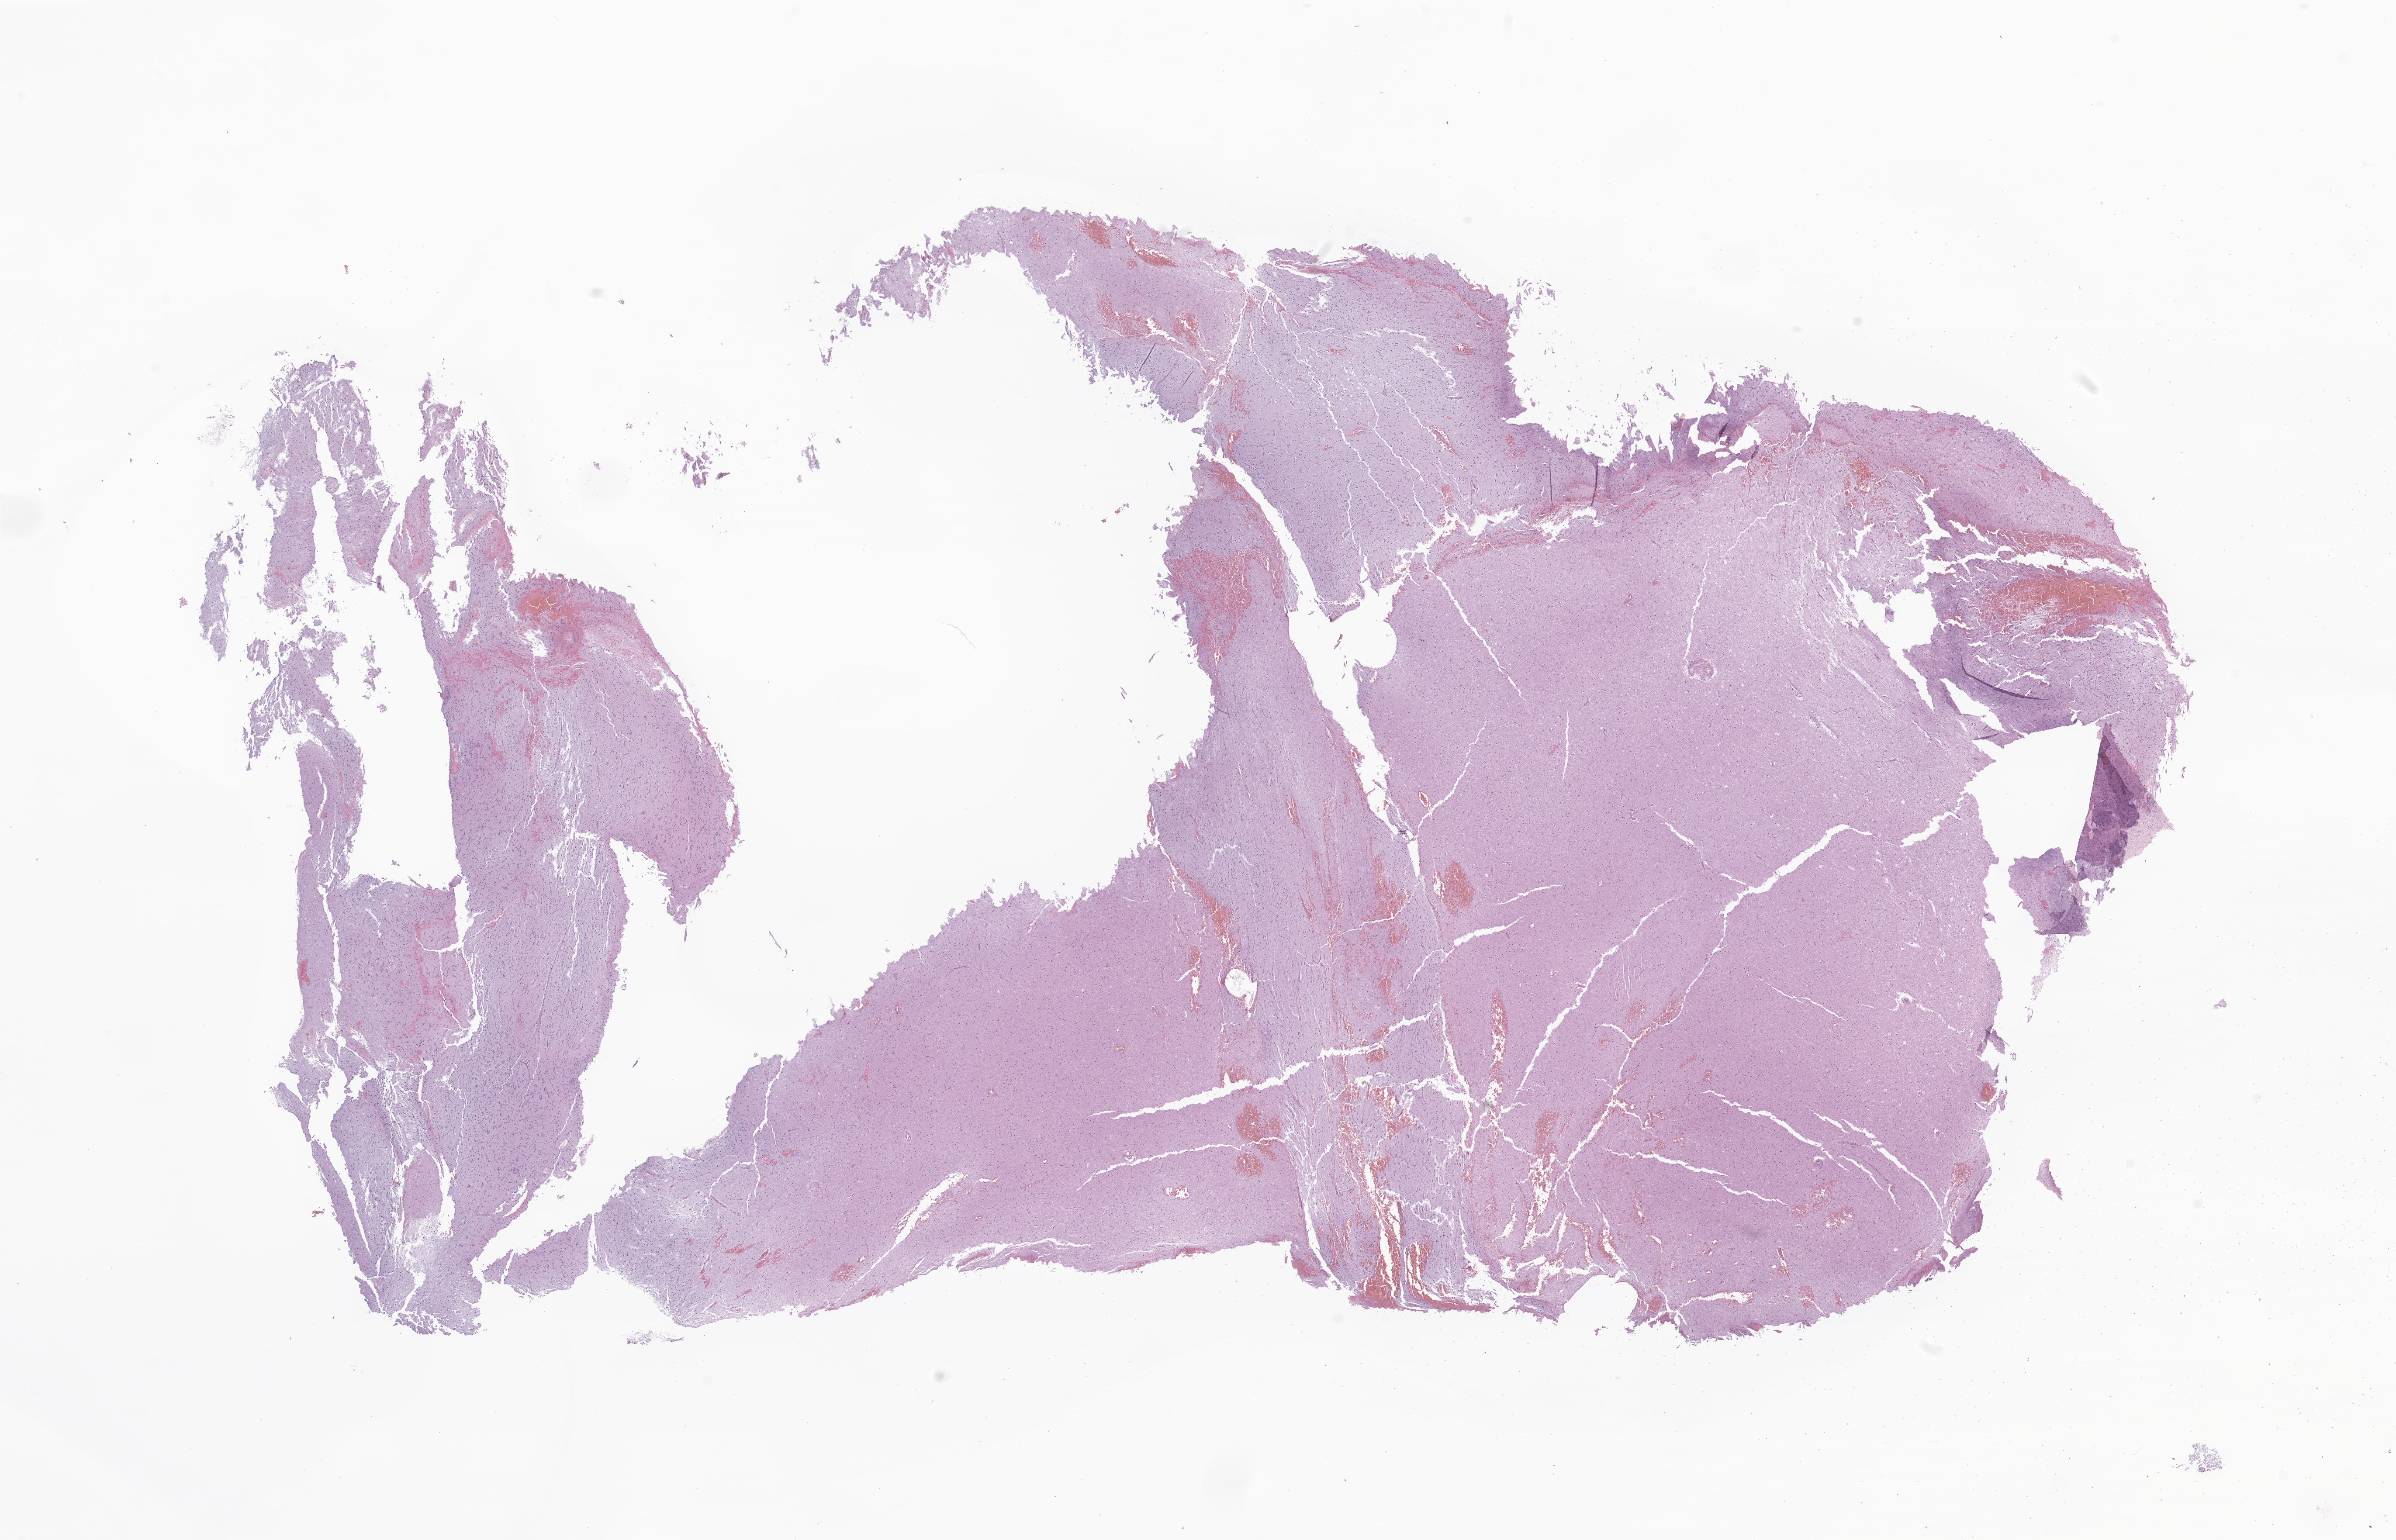
Haematoxylin and eosin whole-slide image of tumor tissue from the frontal lobe — a low-resolution overview of the entire scanned area, about 23.1 x 14.9 mm. Formalin-fixed, paraffin-embedded (FFPE) tissue. Patient male; age 150 months (12 years 6 months).
* diagnosis (ICD-O-3 morphology term): Dysembryoplastic neuroepithelial tumor